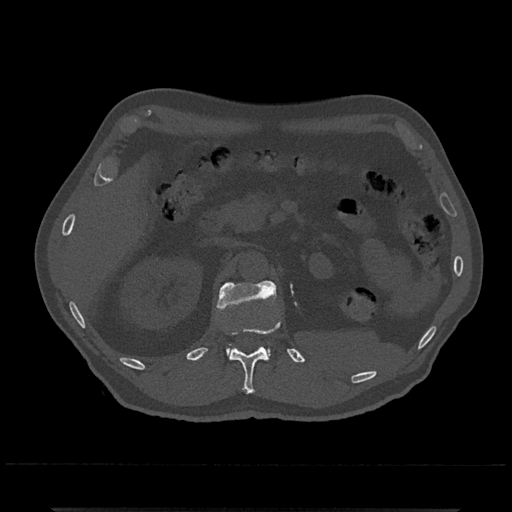
CT including the spine, one axial slice; position 404 of 797 along the scan axis; reconstruction kernel Br40s/3; bone window (W 1800 / L 400 HU); 0.5 mm slice thickness; 512 × 512 image matrix, field of view 393 × 393 mm. Patient: male, 67 years. Case-level facts recorded for this patient, not image findings: primary cancer: prostate.
Annotated regions visible in this slice (semi-automatically segmented with operator editing):
- L1 vertebra: bounding box (x1, y1, x2, y2) in pixels: (217, 280, 277, 360)
- T12 vertebra: (229, 322, 280, 394)